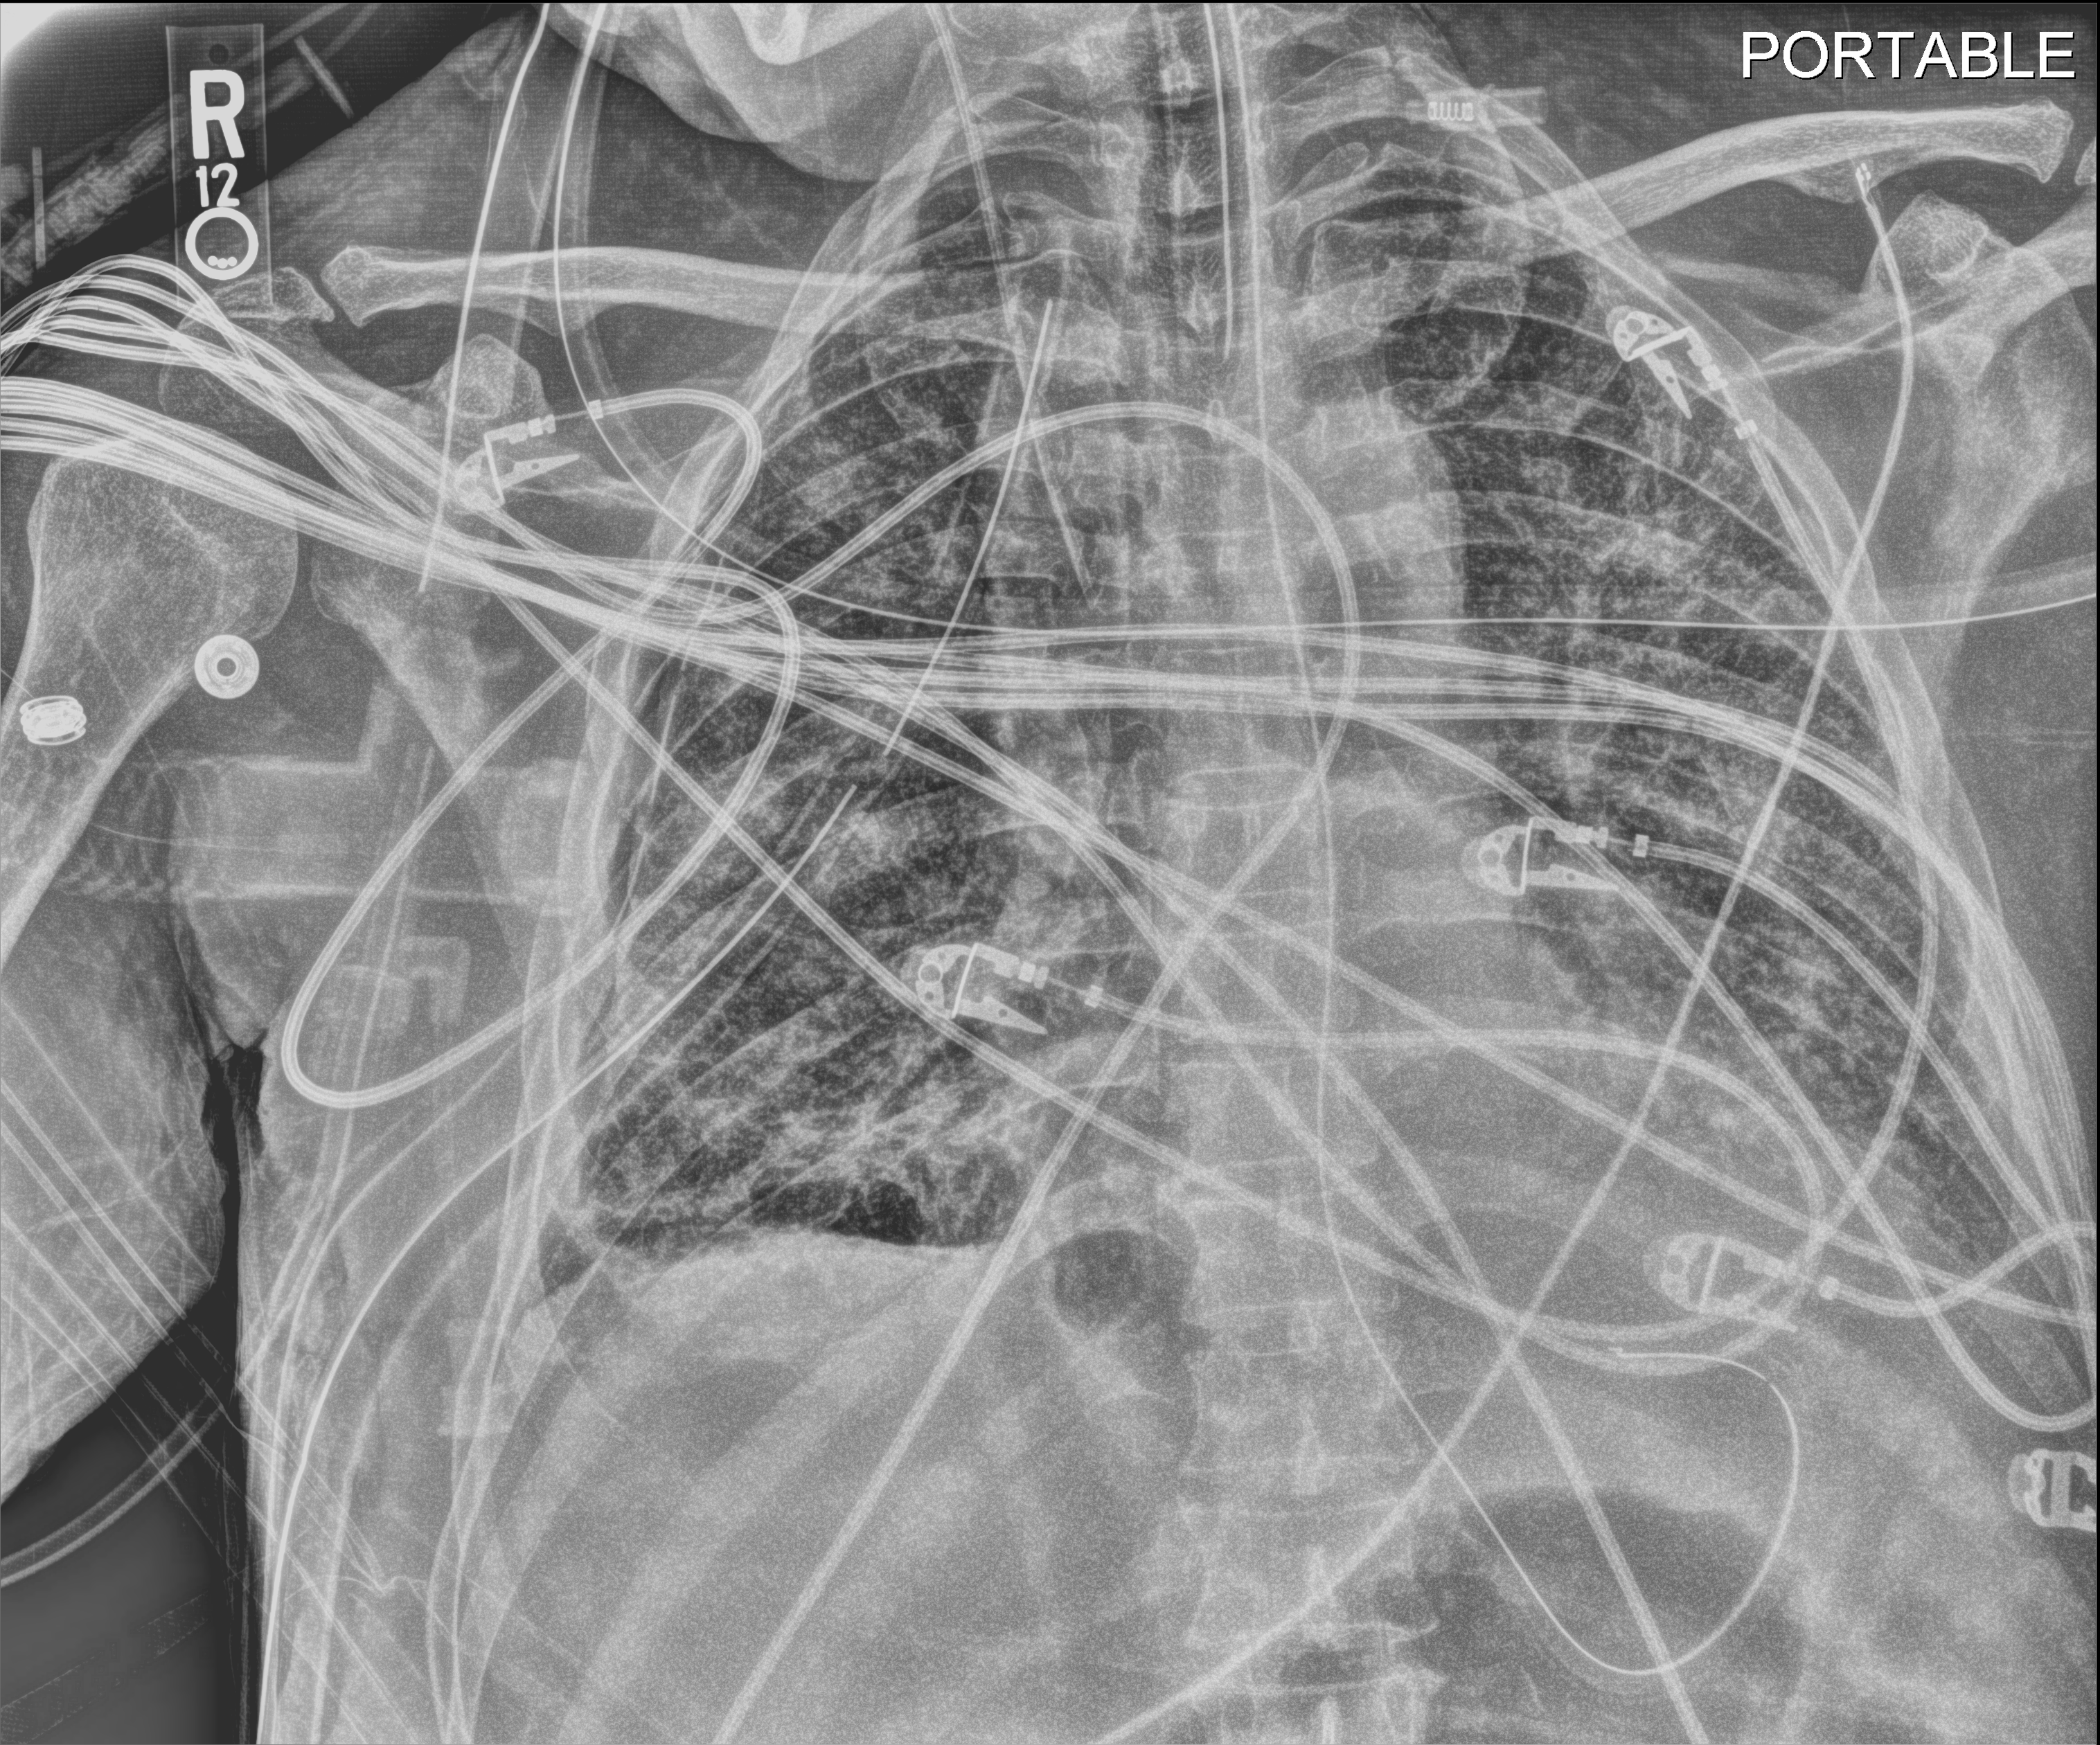
Chest X-ray (portable); anteroposterior (AP) projection. Patient hospitalised with COVID-19; male, aged 60–74 years.
Hospital-stay facts (about this admission, not read from this image; timing relative to this image not recorded): admitted to intensive care during this hospital stay: yes; length of hospital stay: 37 days.